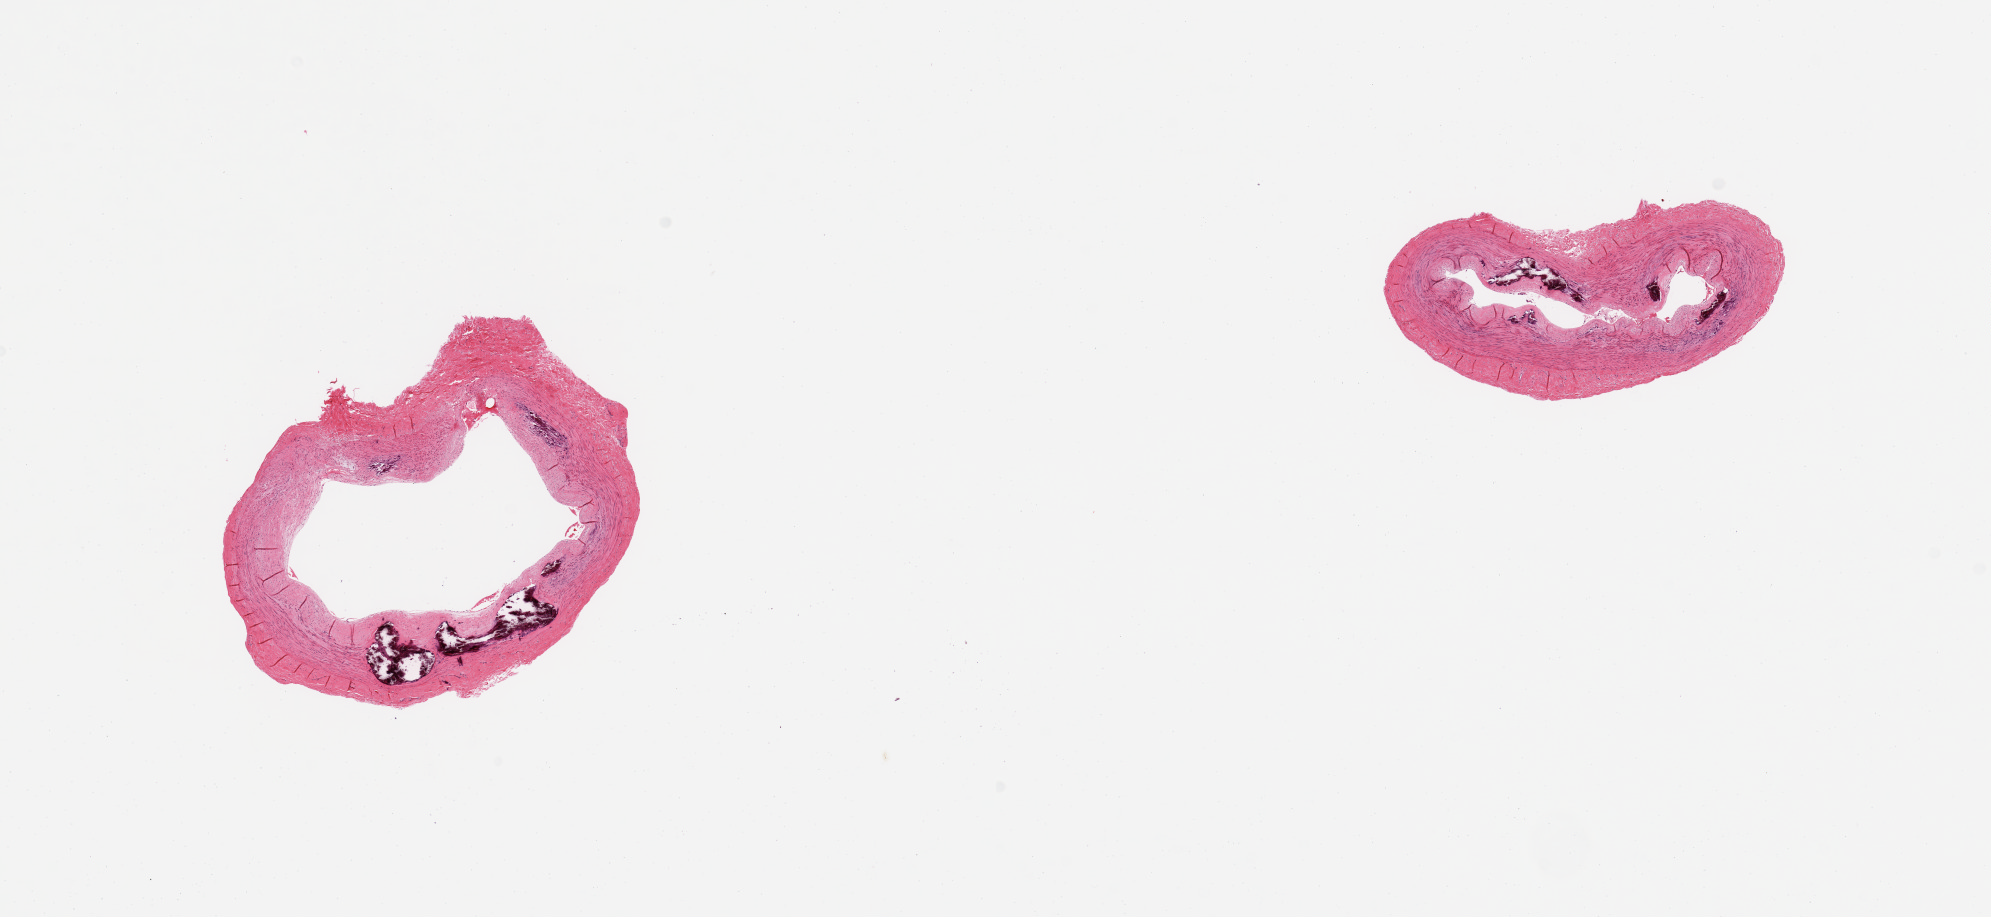
Whole-slide image, haematoxylin and eosin stain, shown as a low-resolution overview of the whole scanned area (about 15.8 x 7.3 mm), PAXgene-fixed, paraffin-embedded tissue, sampled site (target tissue): tibial artery, tissue donor sample. Donor: male.
Pathologist's review note for this sample: 2 pieces; little plaque, but prominent mural calcifications.